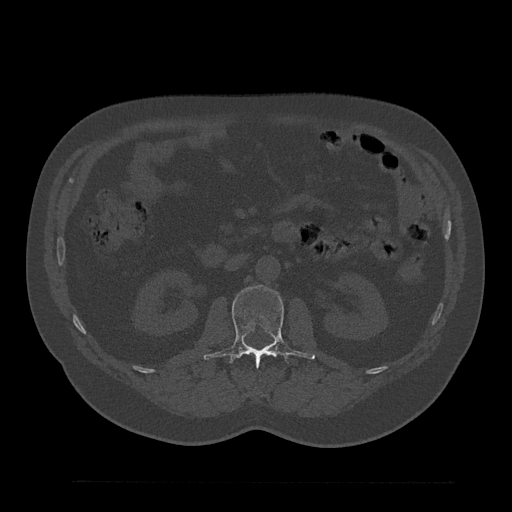
CT including the spine, one axial slice; position 104 of 797 along the scan axis; reconstruction kernel Br40s/3; 120 kVp; bone window (W 1800 / L 400 HU); 0.5 mm slice thickness; 512 × 512 image matrix, field of view 430 × 430 mm. Male patient, age 61 years. Case-level facts recorded for this patient, not image findings: primary cancer: prostate.
Annotated regions visible in this slice (semi-automatic segmentation, software-assisted and operator-edited):
- L1 vertebra: bounding box (x1, y1, x2, y2) in pixels: (263, 353, 272, 356)
- L2 vertebra: (204, 285, 316, 366)